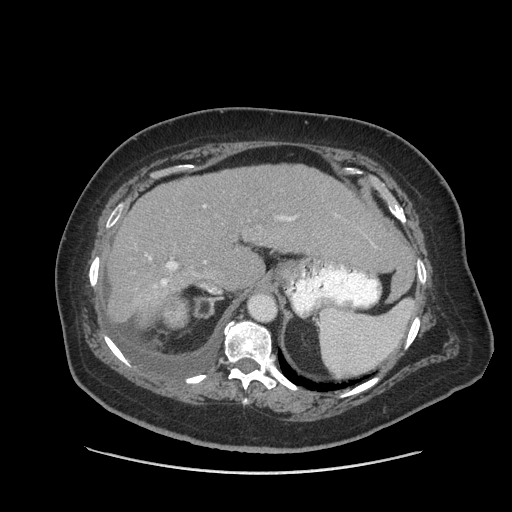
Contrast-enhanced abdominal CT (liver protocol), one axial slice. Position 59 of 91 along the scan axis. 140 kVp. Soft-tissue window (W 400 / L 40 HU). 2.5 mm slice thickness. 512 × 512 image matrix, field of view 420 × 420 mm. From the clinical record (not read from this slice): diagnosis: hepatocellular carcinoma (patient treated with transarterial chemoembolisation; whether this scan precedes or follows treatment is not stated here); TNM stage (as recorded): Stage-I; Child-Pugh class: A; tumour differentiation: well differentiated; tumour nodularity: uninodular.
Structures marked on this image (semi-automatic segmentation, software-assisted and operator-edited):
- liver parenchyma outside the tumour (the mass and vessels are separate outlines, so this box may not span the whole liver): bounding box <104,164,404,320> (left, top, right, bottom; pixels)
- mass: <166,304,187,325>
- liver vessels: <148,205,295,288>